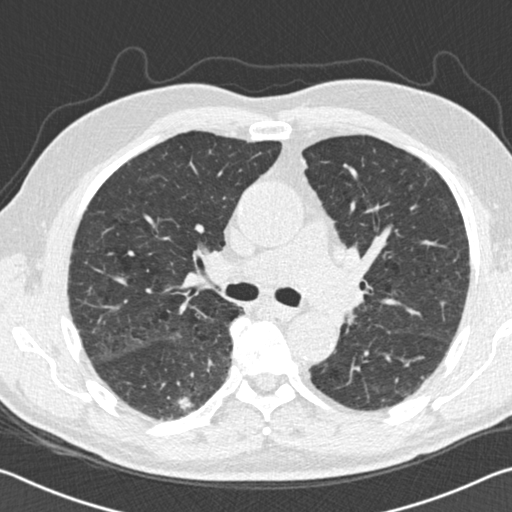
Chest CT (low-dose screening protocol), one axial image. Second screening round (one year after baseline). Lung window (W 1500 / L -600 HU). Male participant, aged 69 years at enrolment. Current smoker at enrolment.
- Expert reader's lesion annotation, box from (x=160, y=377) to (x=208, y=425) px.
- Reader record for this screening exam (exam-level; its link to the box is not recorded): non-calcified nodule or mass ≥4 mm, right lower lobe, 10 × 10 mm, spiculated (stellate) margins, soft tissue attenuation, pre-existing on the prior screen: yes; interval growth: yes.
- Later outcome: lung cancer diagnosed 290 days after this screen — squamous cell carcinoma, NOS, right lower lobe, moderately differentiated (G2), stage IA (AJCC 6th edition), 25 mm at pathology.